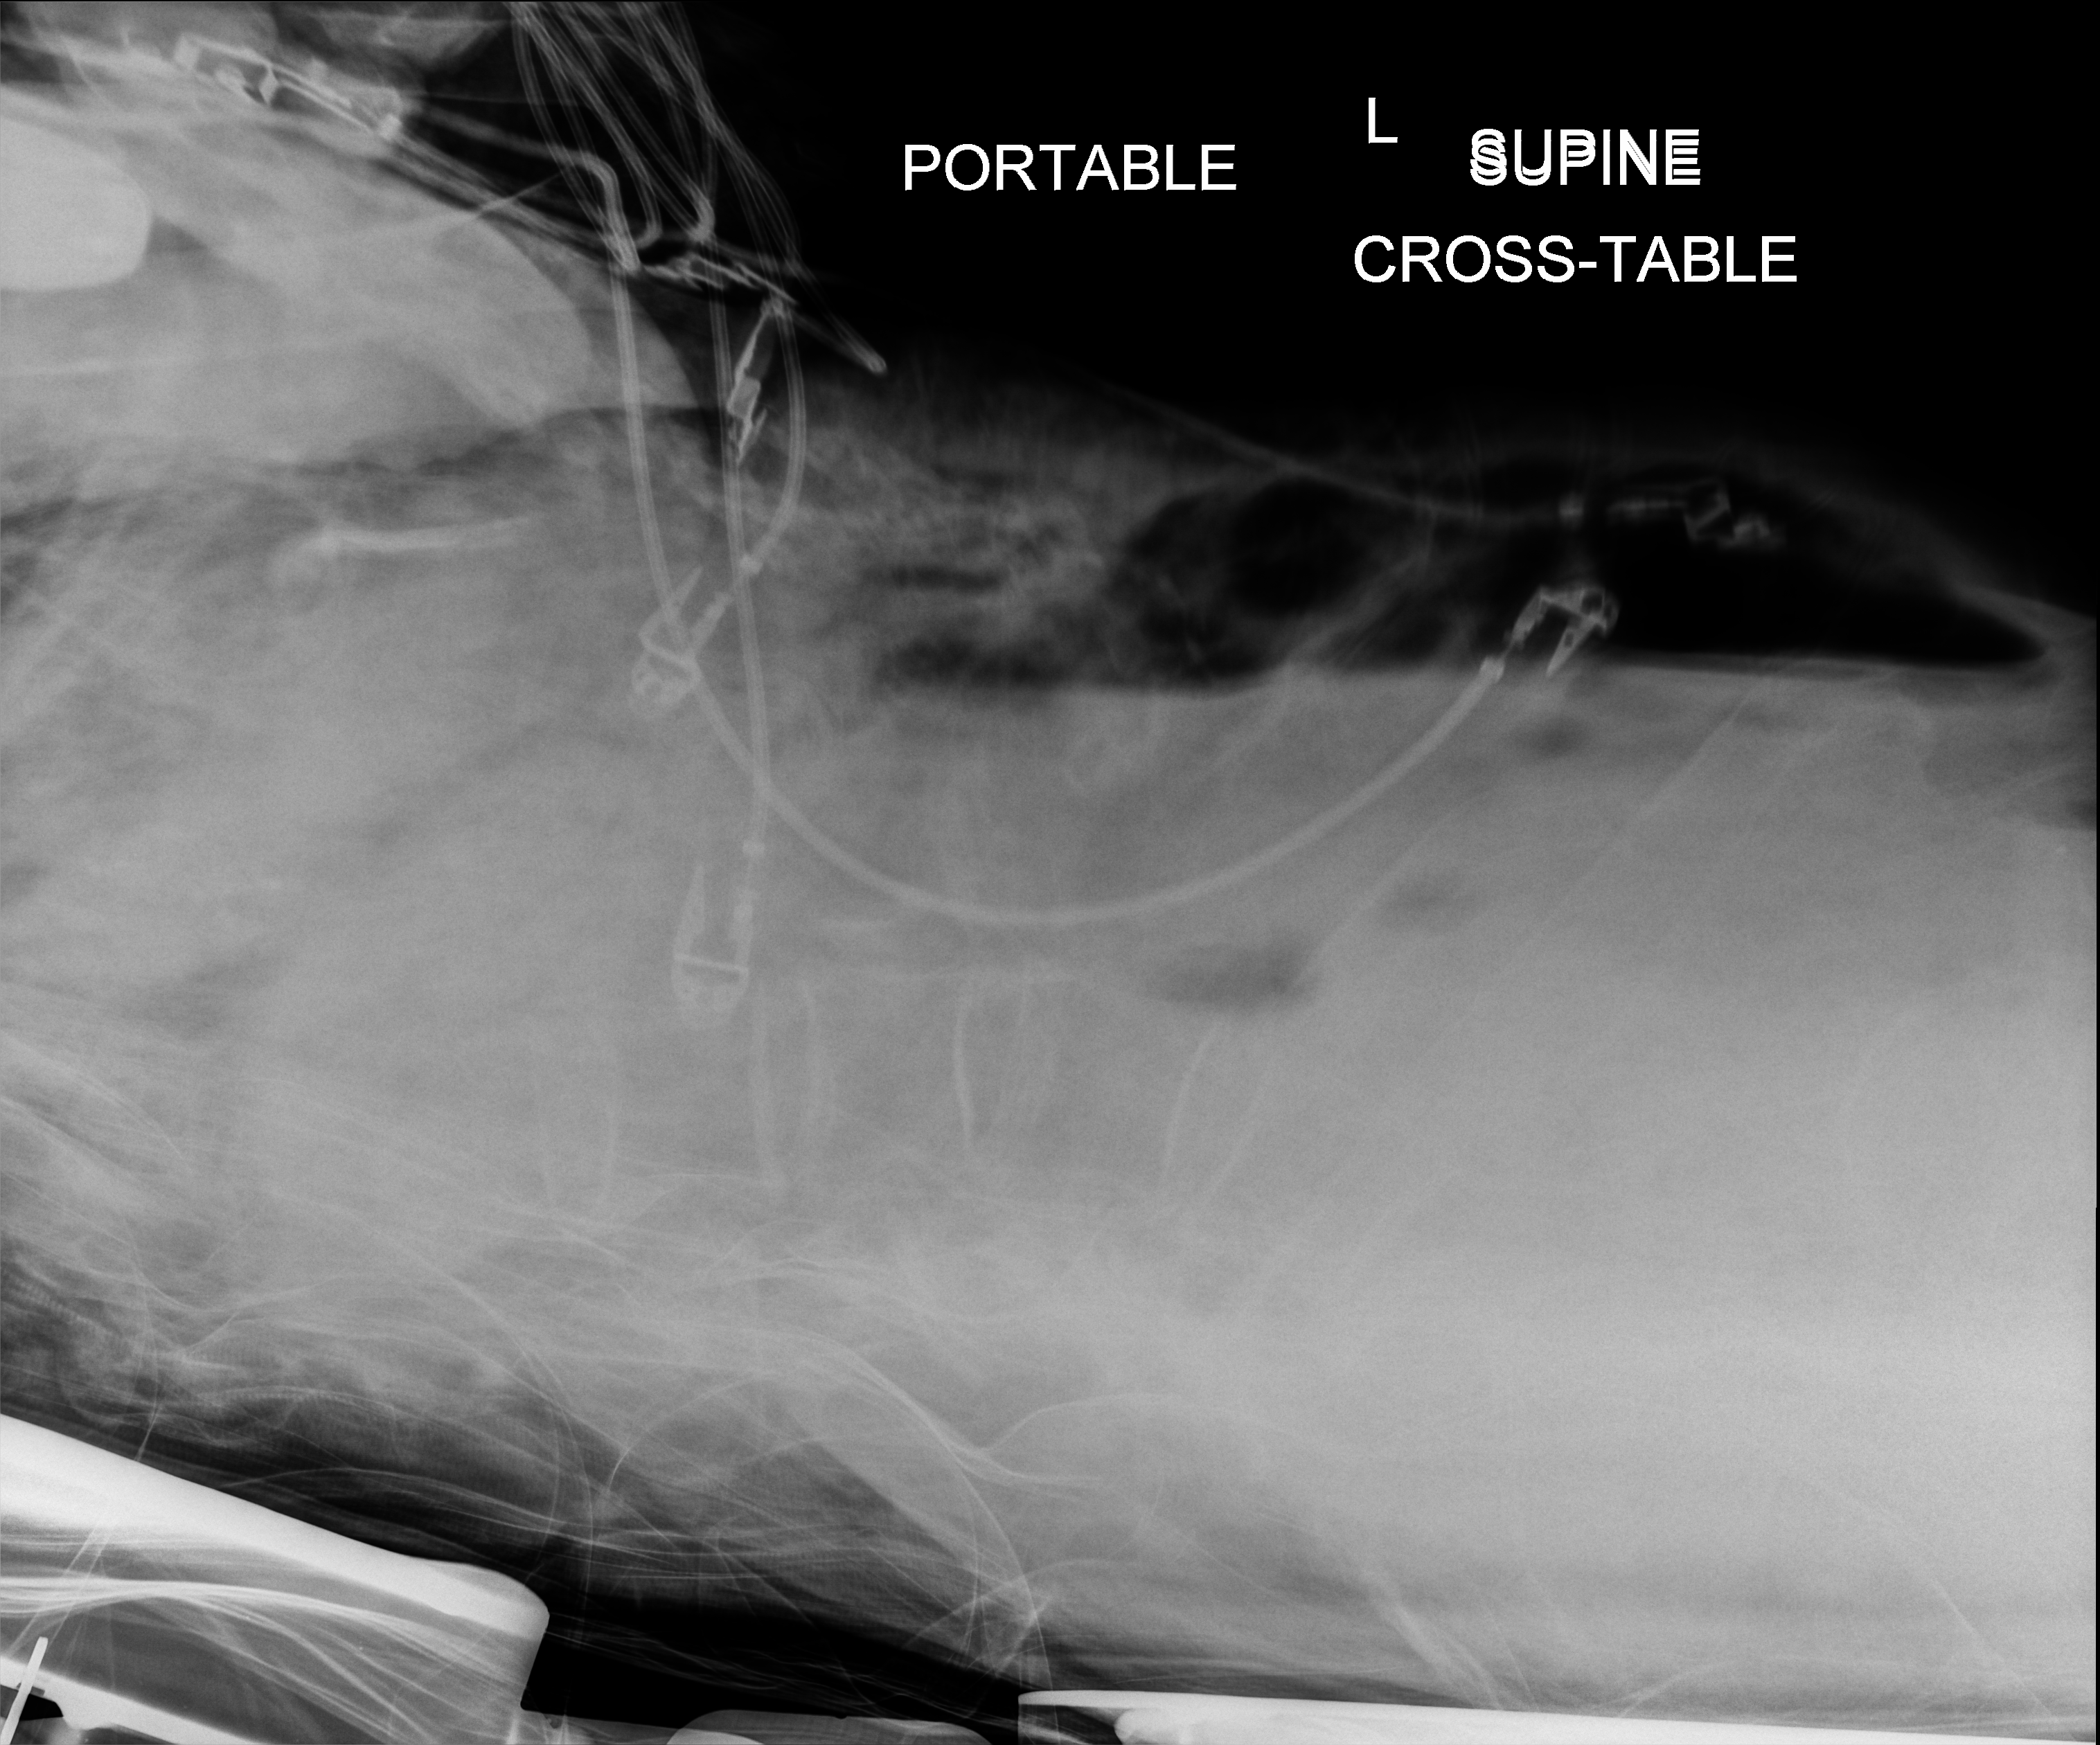
Portable abdomen radiograph; anteroposterior (AP) projection. Patient hospitalised with COVID-19; female, aged 75–90 years.
Hospital-stay facts (about this admission, not read from this image; timing relative to this image not recorded):
- COPD (admission record): no
- hypertension (admission record): yes
- length of hospital stay: 3 days